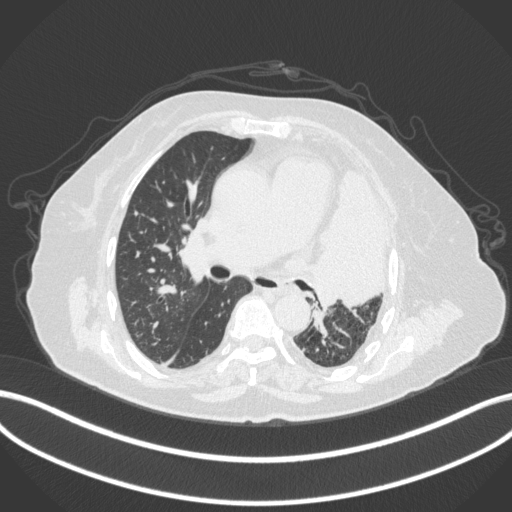
Chest CT, one axial slice; slice 219 of 399 in the series (ordered by position); reconstruction kernel B31f; lung window (W 1500 / L -600 HU); 512 × 512 image matrix. Patient: female, 75 years. Case-level facts recorded for this patient, not image findings: clinical TNM (as recorded): T3 N3 M1.
Annotated regions visible in this slice (bounding box drawn by a radiologist):
- lung tumour (recorded histology: adenocarcinoma): bounding box (x1, y1, x2, y2) in pixels: (304, 162, 390, 314)